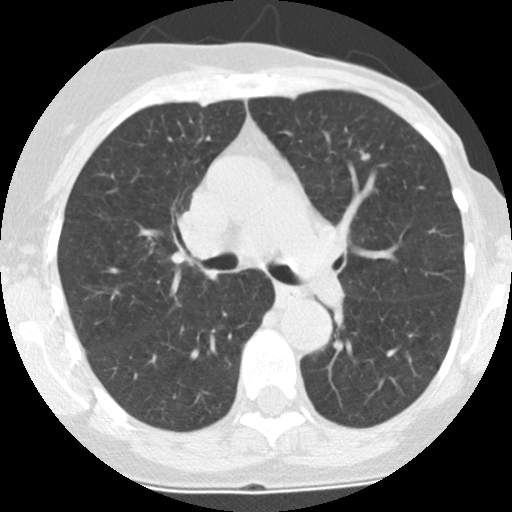
Axial slice from a low-dose chest CT screening exam, baseline screening round, lung window (W 1500 / L -600 HU), 2.5 mm slice thickness, standard (soft-tissue) reconstruction kernel (STANDARD), 120 kVp, slice 93 of 225 in the series. Female participant, aged 66 years at enrolment. Former smoker at enrolment.
Expert-annotated lung lesion, box from (x=358, y=146) to (x=374, y=166) px. No non-calcified nodule or mass ≥4 mm was recorded by the screening reader at this exam. Official screen result: negative screen, minor abnormalities not suspicious for lung cancer.